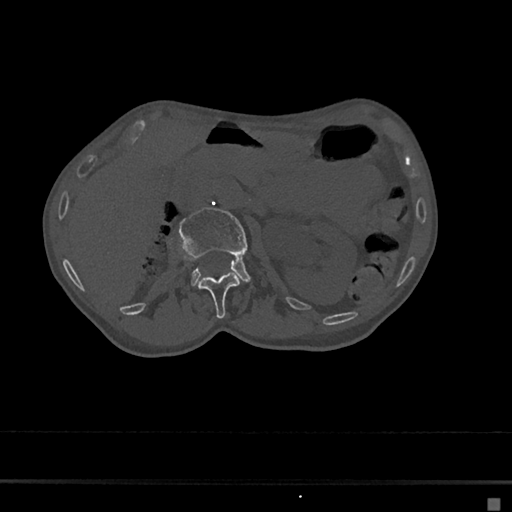
CT including the spine, one axial slice. Position 46 of 797 along the scan axis. 120 kVp. Bone window (W 1800 / L 400 HU). 0.5 mm slice thickness. 512 × 512 image matrix. Patient: female, 68 years. From the clinical record (not read from this slice): primary cancer: renal.
Structures marked on this image (semi-automatically segmented with operator editing):
- L1 vertebra: box from (x=198, y=273) to (x=239, y=319) px
- L2 vertebra: (x=179, y=207)–(x=249, y=285)